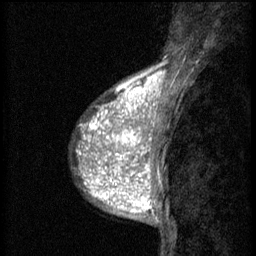
Breast MRI (dynamic contrast-enhanced), one sagittal slice; position 19 of 60 along the scan axis; 3 images stored at this slice position (order not interpretable as contrast timing); 1.5 T; TE 4.2 ms, TR 8.2 ms; 256 × 256 image matrix, field of view 180 × 180 mm. Female patient, age 38 years.
Annotated regions visible in this slice (semi-automatically segmented with operator editing):
- analysis volume of interest (the breast-tissue region the enhancement analysis was run in; not a lesion): bounding box (x1, y1, x2, y2) in pixels: (92, 112, 152, 171)
- tumour enhancement mask (voxels above the 70 % enhancement threshold inside the analysis volume of interest): (92, 112, 152, 171)